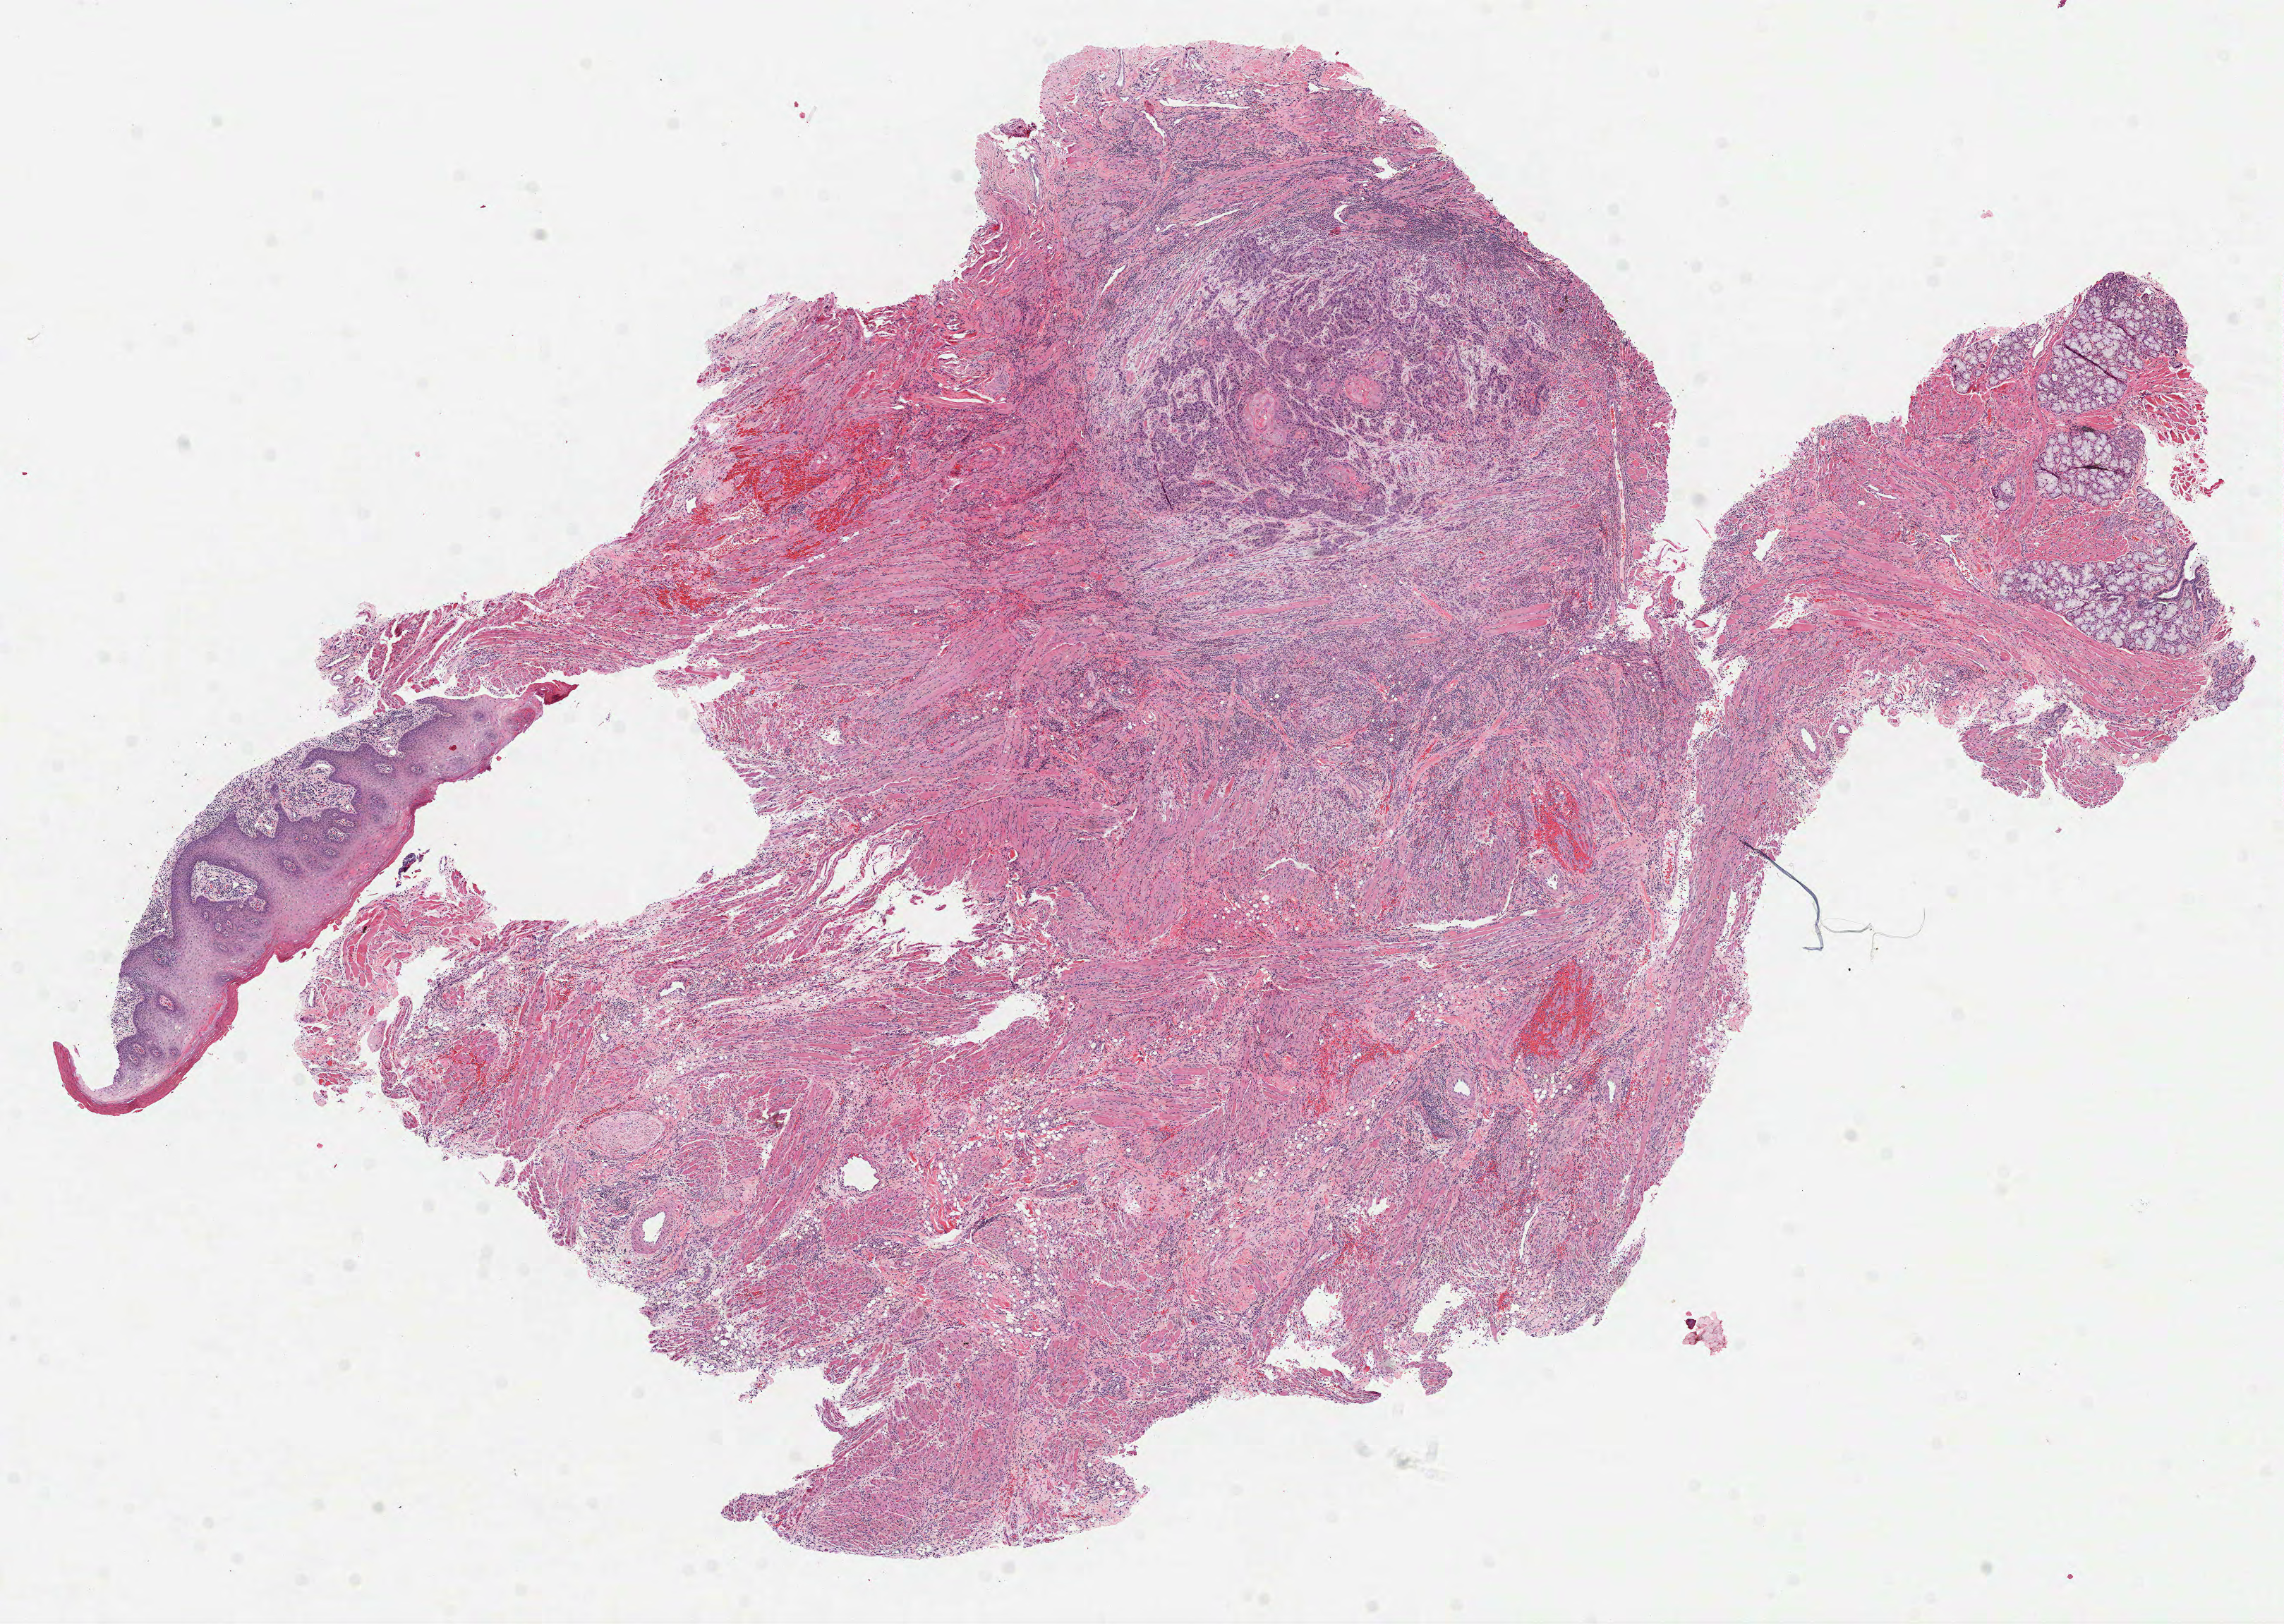
Digitized H&E-stained tissue section (whole slide) — whole scanned area (about 13.1 x 9.3 mm, from a 40x scan) shown as a low-resolution overview; FFPE section; sample: primary tumour, head and neck. Patient: male, age at initial diagnosis 53 years. Histologic grade: G2 (moderately differentiated).
- AJCC pathologic stage: IVA (7th edition)
- histologic diagnosis: Squamous cell carcinoma, NOS (tongue, NOS)
- TNM: T3 N2b
- lymph nodes positive (case pathology): 2 of 26 examined